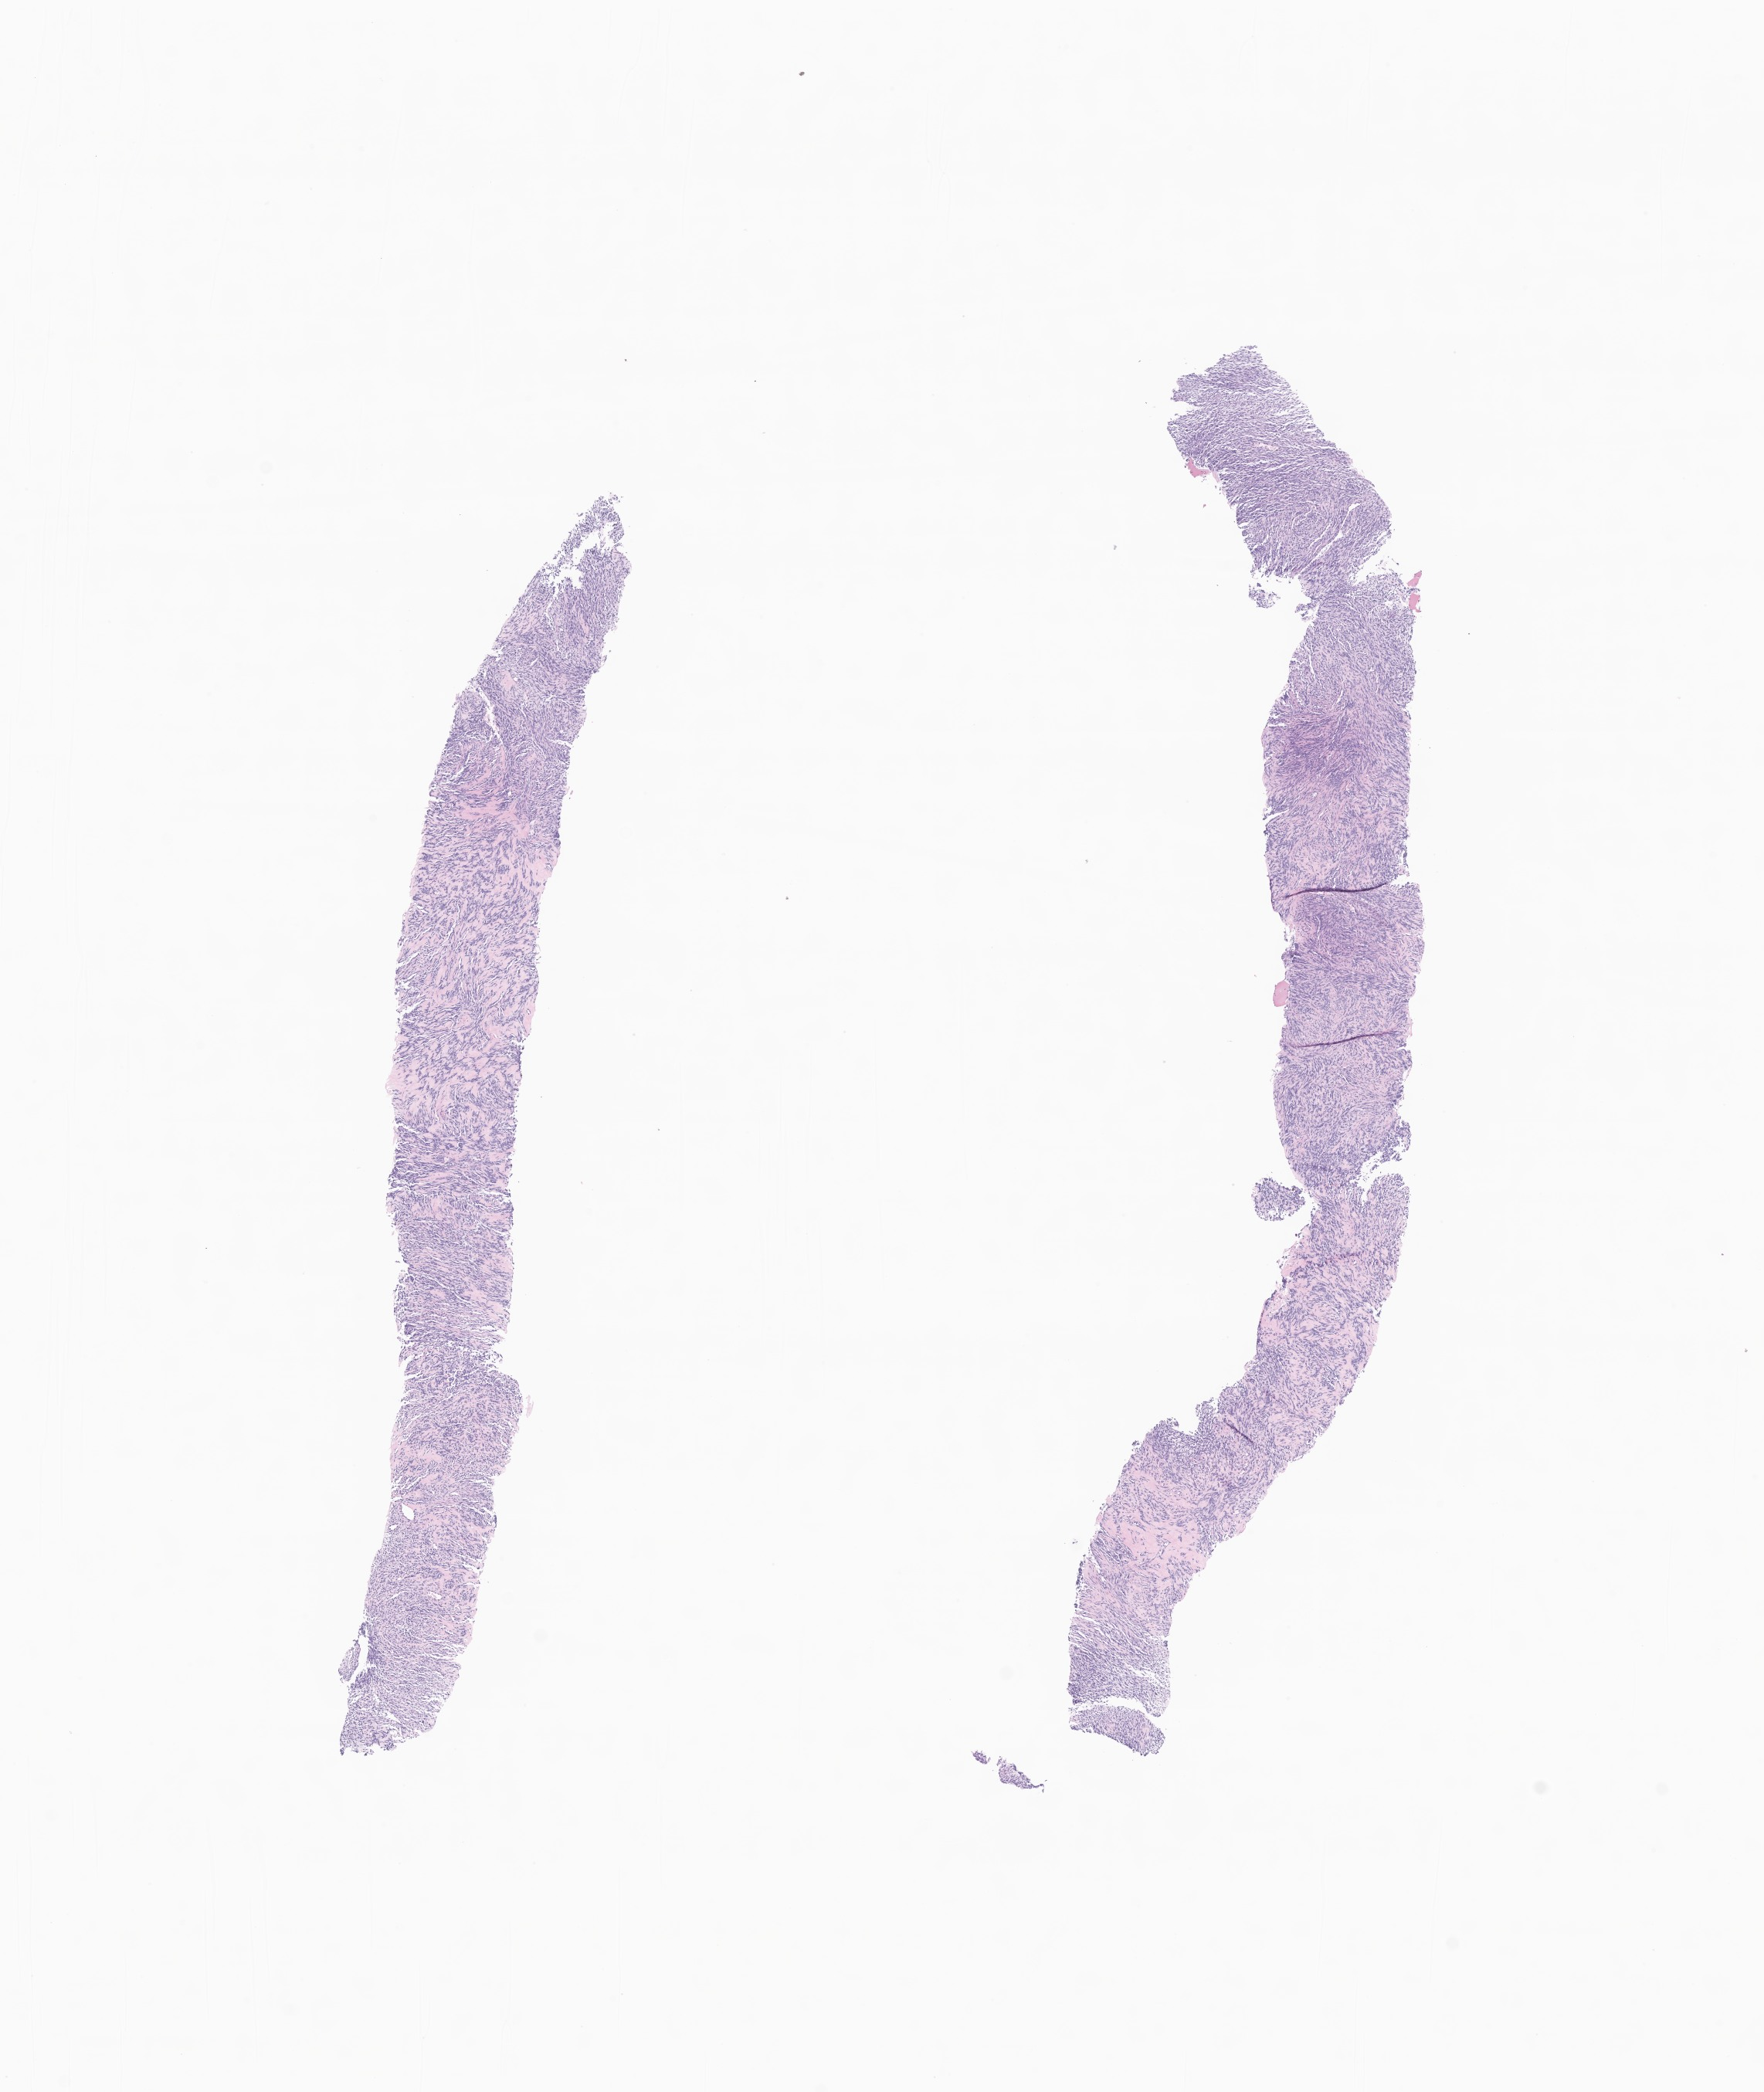
H&E whole-slide image of tumor tissue from the thorax — whole scanned area (about 9.6 x 11.4 mm) shown as a low-resolution overview. Formalin-fixed, paraffin-embedded (FFPE) tissue. Patient: male, age 306 months.
Diagnosis (ICD-O-3 morphology term): Spindle cell rhabdomyosarcoma.